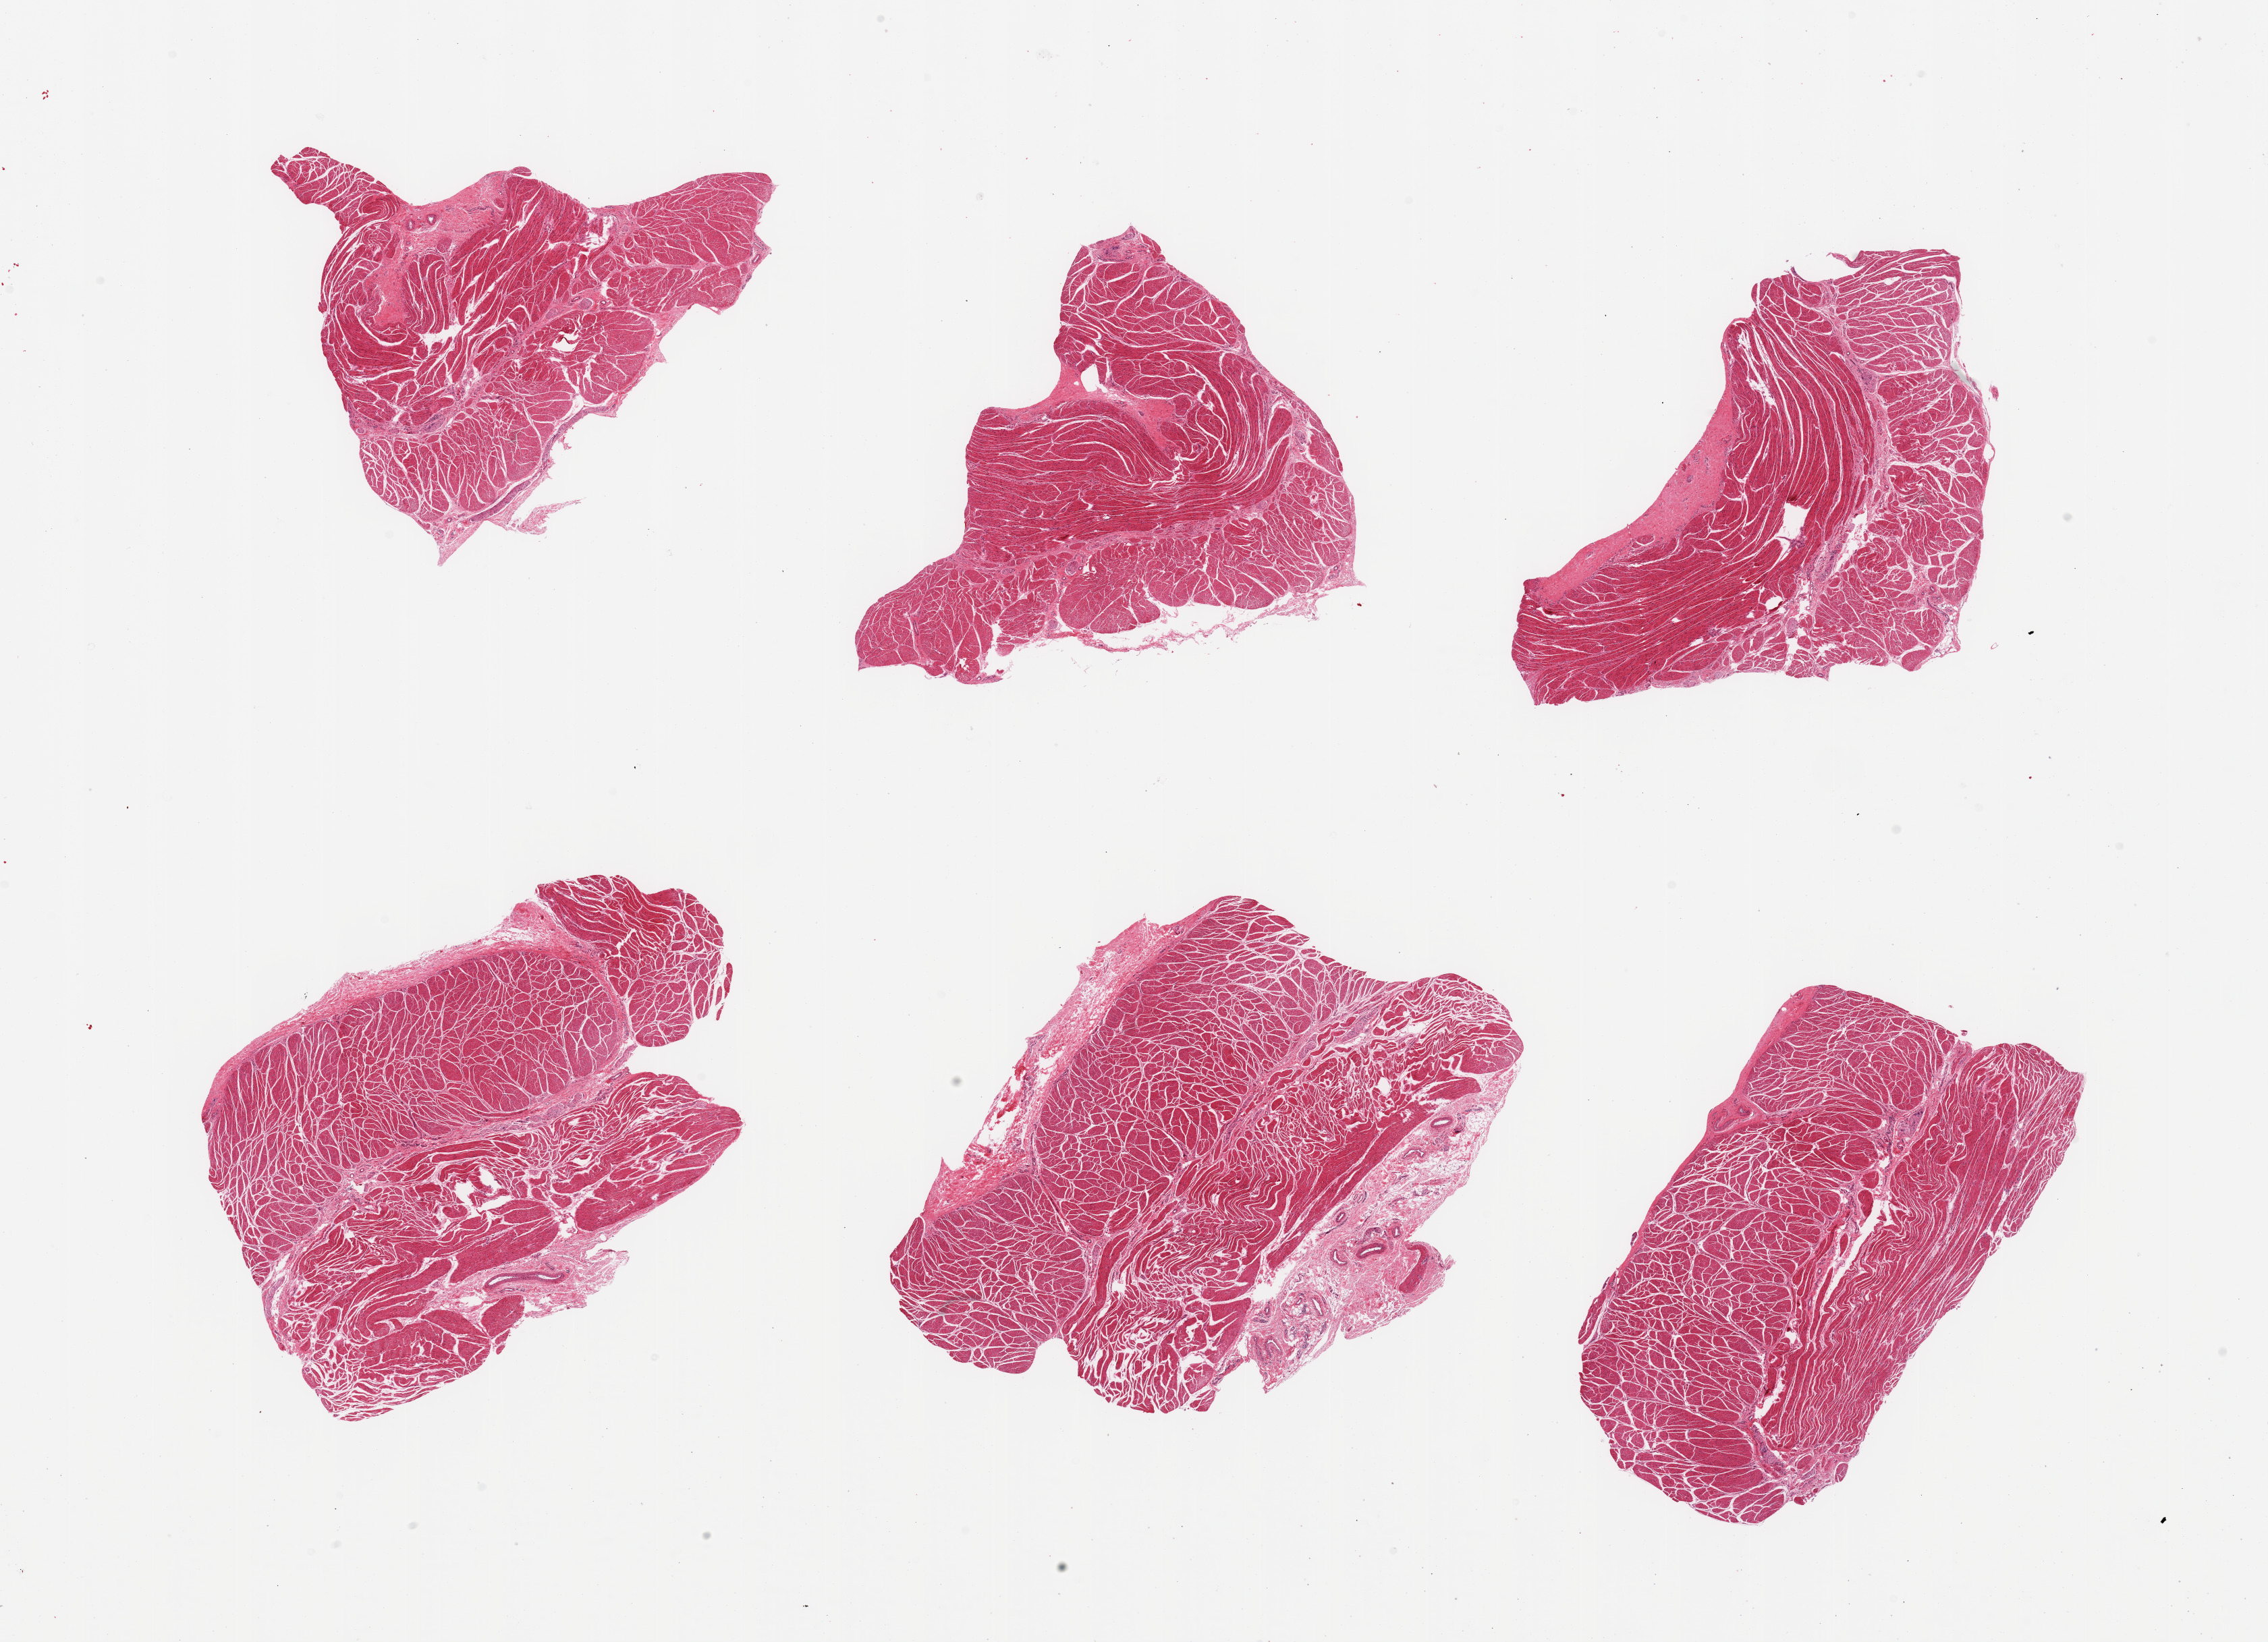
Whole-slide image, hematoxylin and eosin (H&E) stain — low-resolution overview of the scanned area, about 26.6 x 19.2 mm (acquisition: 20x scan), PAXgene-fixed, paraffin-embedded tissue, target tissue: esophageal muscle, tissue donor sample. Male donor.
Reviewer comment on this tissue sample: 6 pieces; well dissected muscle with slight stromal content.